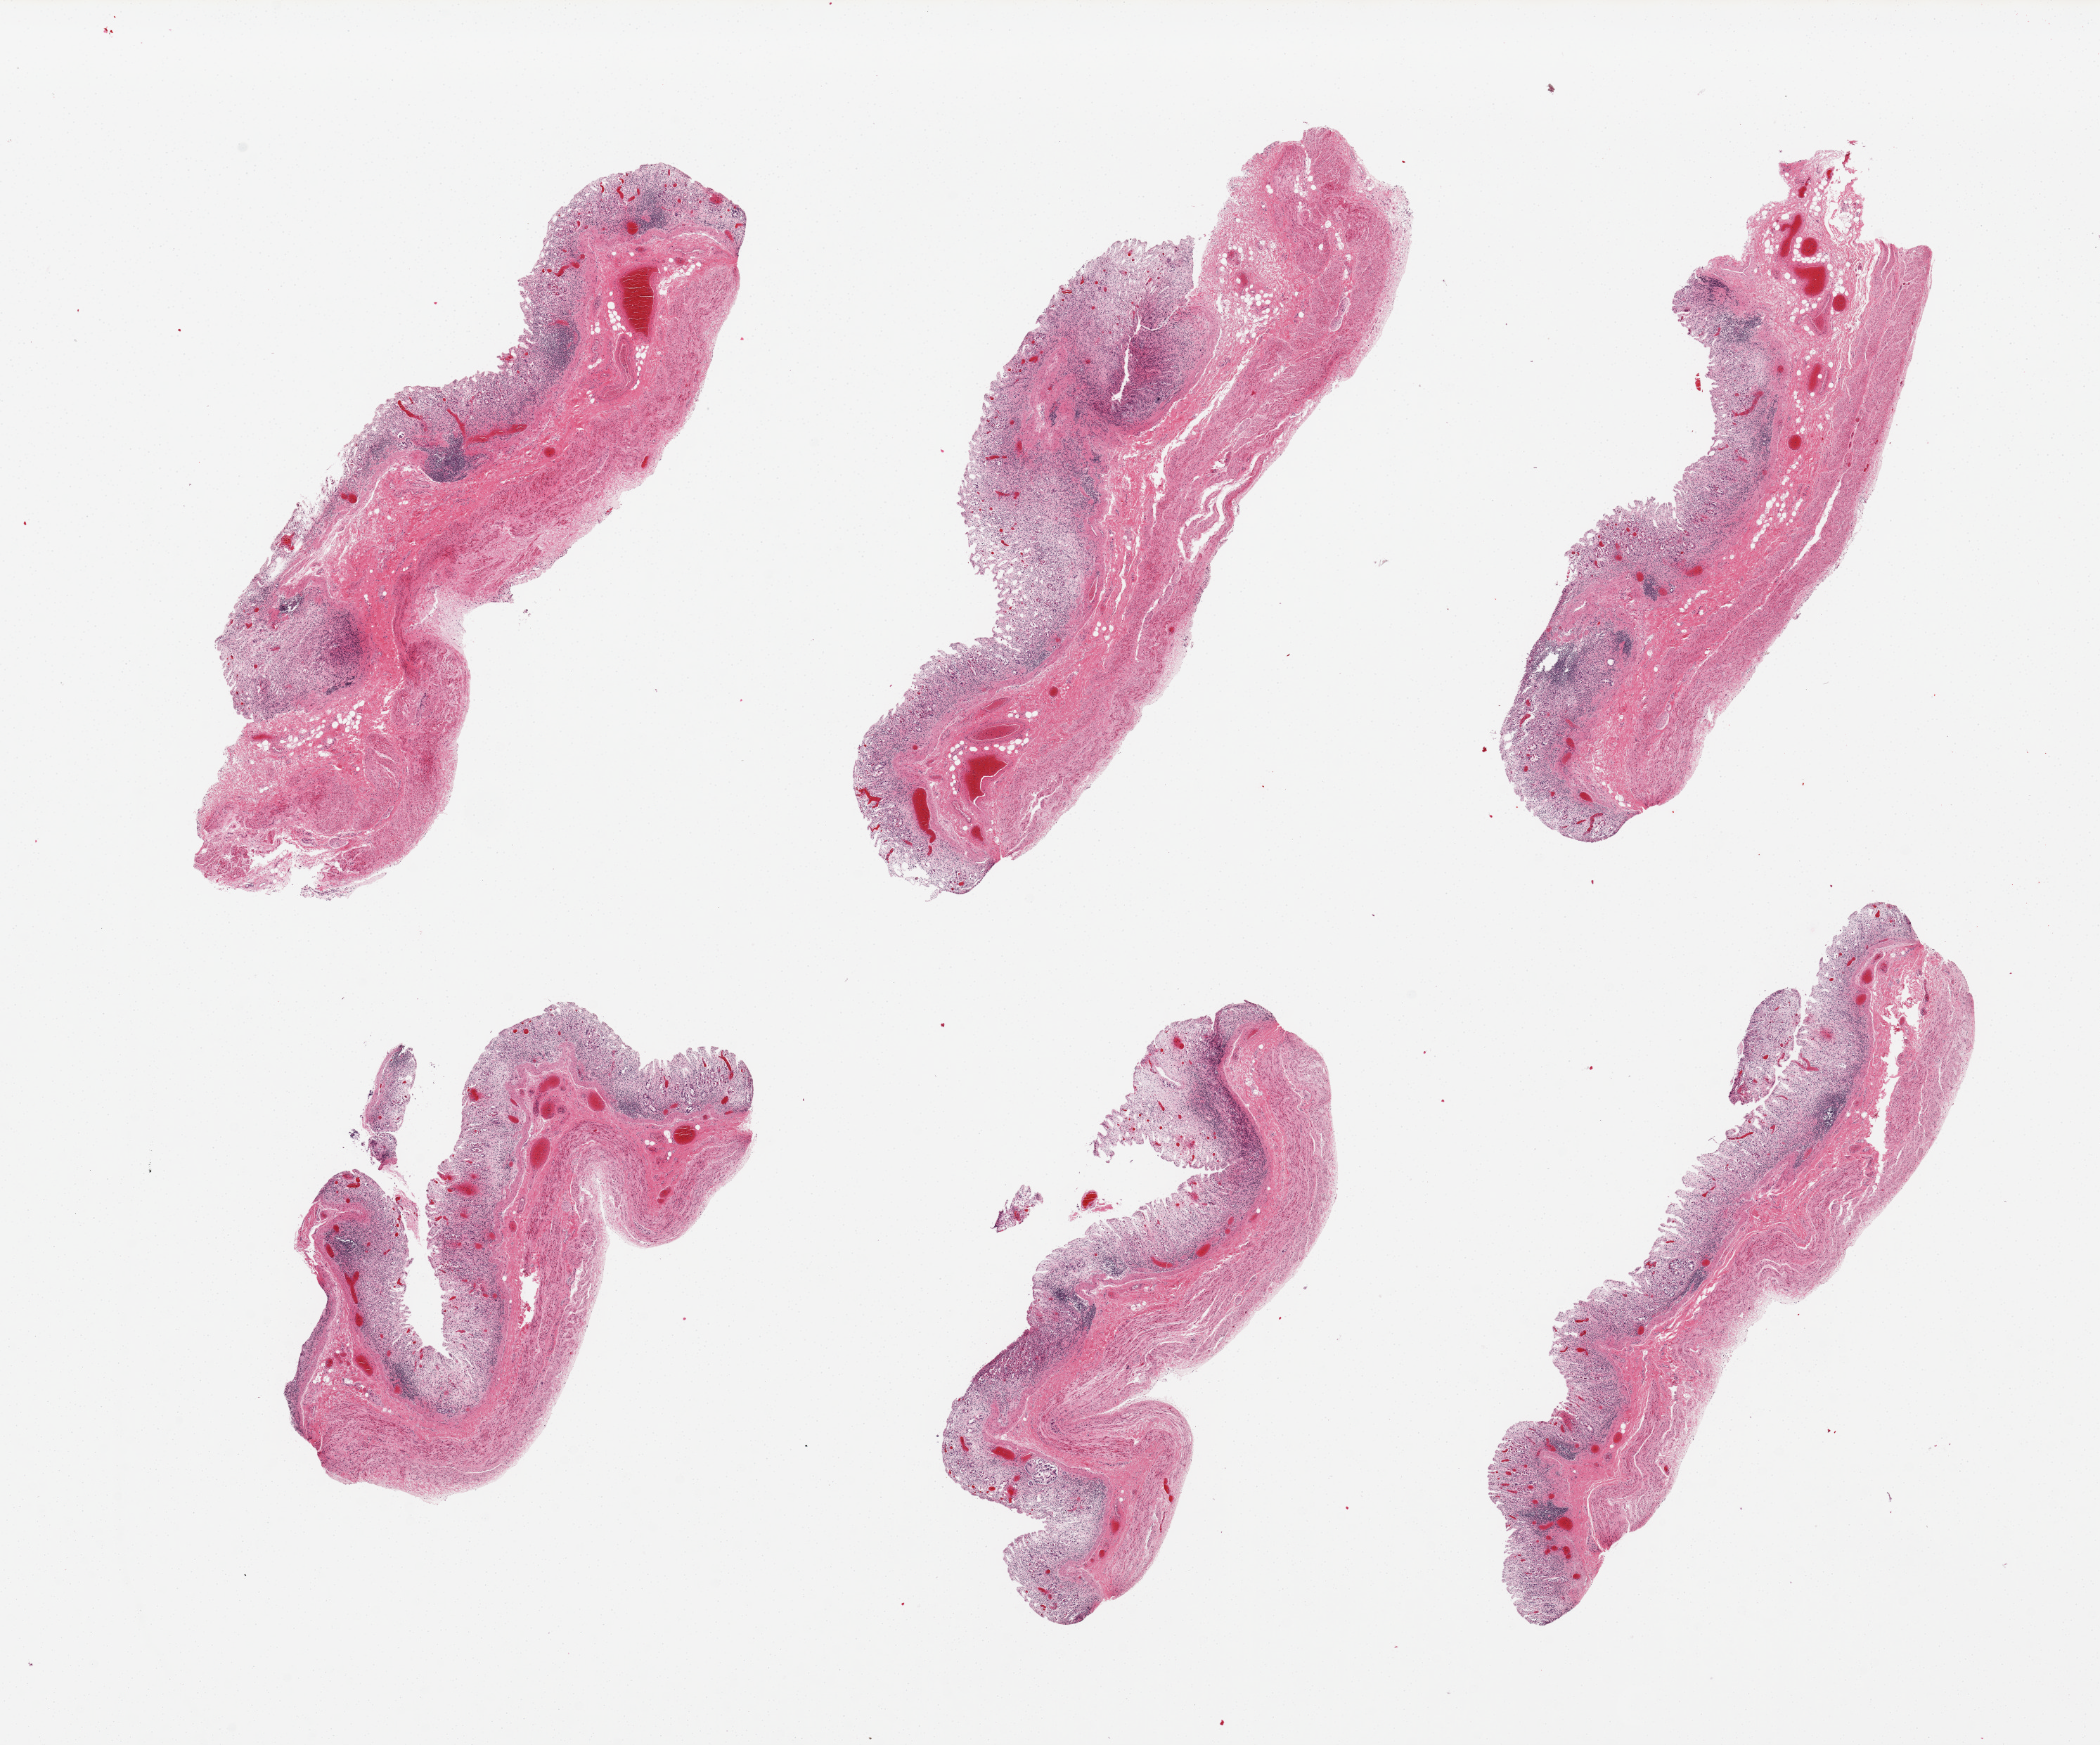
Haematoxylin and eosin whole-slide image, a low-resolution overview of the entire scanned area, about 23.6 x 19.6 mm (slide scanned at 20x), PAXgene-fixed paraffin-embedded (PFPE) section, section of stomach (target tissue), donor tissue sample.
Reviewer comment on this tissue sample: 6 pieces; mucosa is 20-30% thickness, but badly autolzyed/sloughed.